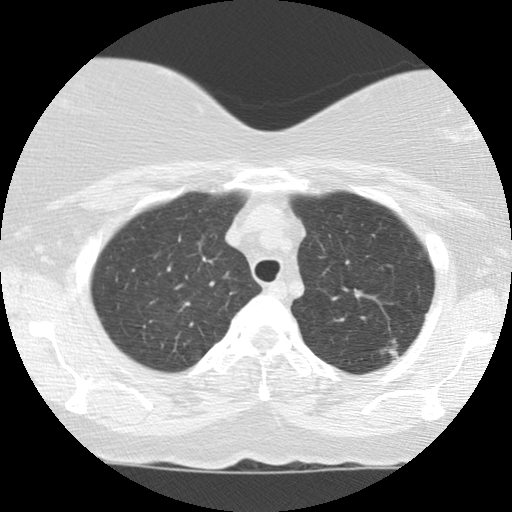
Axial slice from a low-dose chest CT screening exam; baseline screening round; lung window (W 1500 / L -600 HU); 120 kVp; 512 × 512 image matrix. Female, age 56 years at enrolment. Current smoker at enrolment.
- Expert reader's lesion annotation, bounding box [x1, y1, x2, y2] px = [355, 319, 419, 384].
- The screening reader recorded 4 non-calcified nodules or masses ≥4 mm on this exam (left upper lobe, left upper lobe, right upper lobe, left upper lobe); which of them this box marks is not recorded.
- Later outcome: lung cancer diagnosed 798 days after this screen (after the third annual screen) — adenocarcinoma, NOS, left upper lobe, moderately differentiated (G2), stage IA (AJCC 6th edition), 10 mm at pathology.